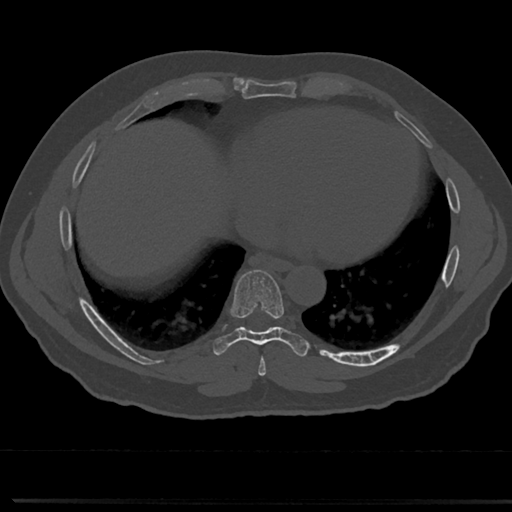
CT including the spine, one axial slice; position 356 of 817 along the scan axis; 120 kVp; bone window (W 1800 / L 400 HU); 0.5 mm slice thickness; 512 × 512 image matrix, field of view 355 × 355 mm. Patient: male, 61 years. Case-level facts recorded for this patient, not image findings: primary cancer: prostate.
Annotated regions visible in this slice (semi-automatic segmentation, software-assisted and operator-edited):
- T7 vertebra: bounding box <240,329,283,363> (left, top, right, bottom; pixels)
- T8 vertebra: <237,270,284,336>